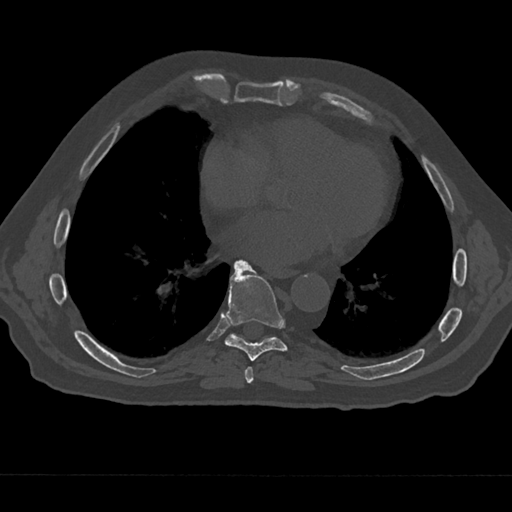
CT including the spine, one axial slice. Slice 309 of 797 in the series (ordered by position). Bone window (W 1800 / L 400 HU). 512 × 512 image matrix, field of view 377 × 377 mm. Male patient, age 75 years. Case-level facts recorded for this patient, not image findings: primary cancer: renal; vertebrae with lytic lesions (as recorded): T4.
Structures marked on this image (semi-automatic segmentation, software-assisted and operator-edited):
- T7 vertebra: bounding box <238,366,254,384> (left, top, right, bottom; pixels)
- T8 vertebra: <224,260,288,361>